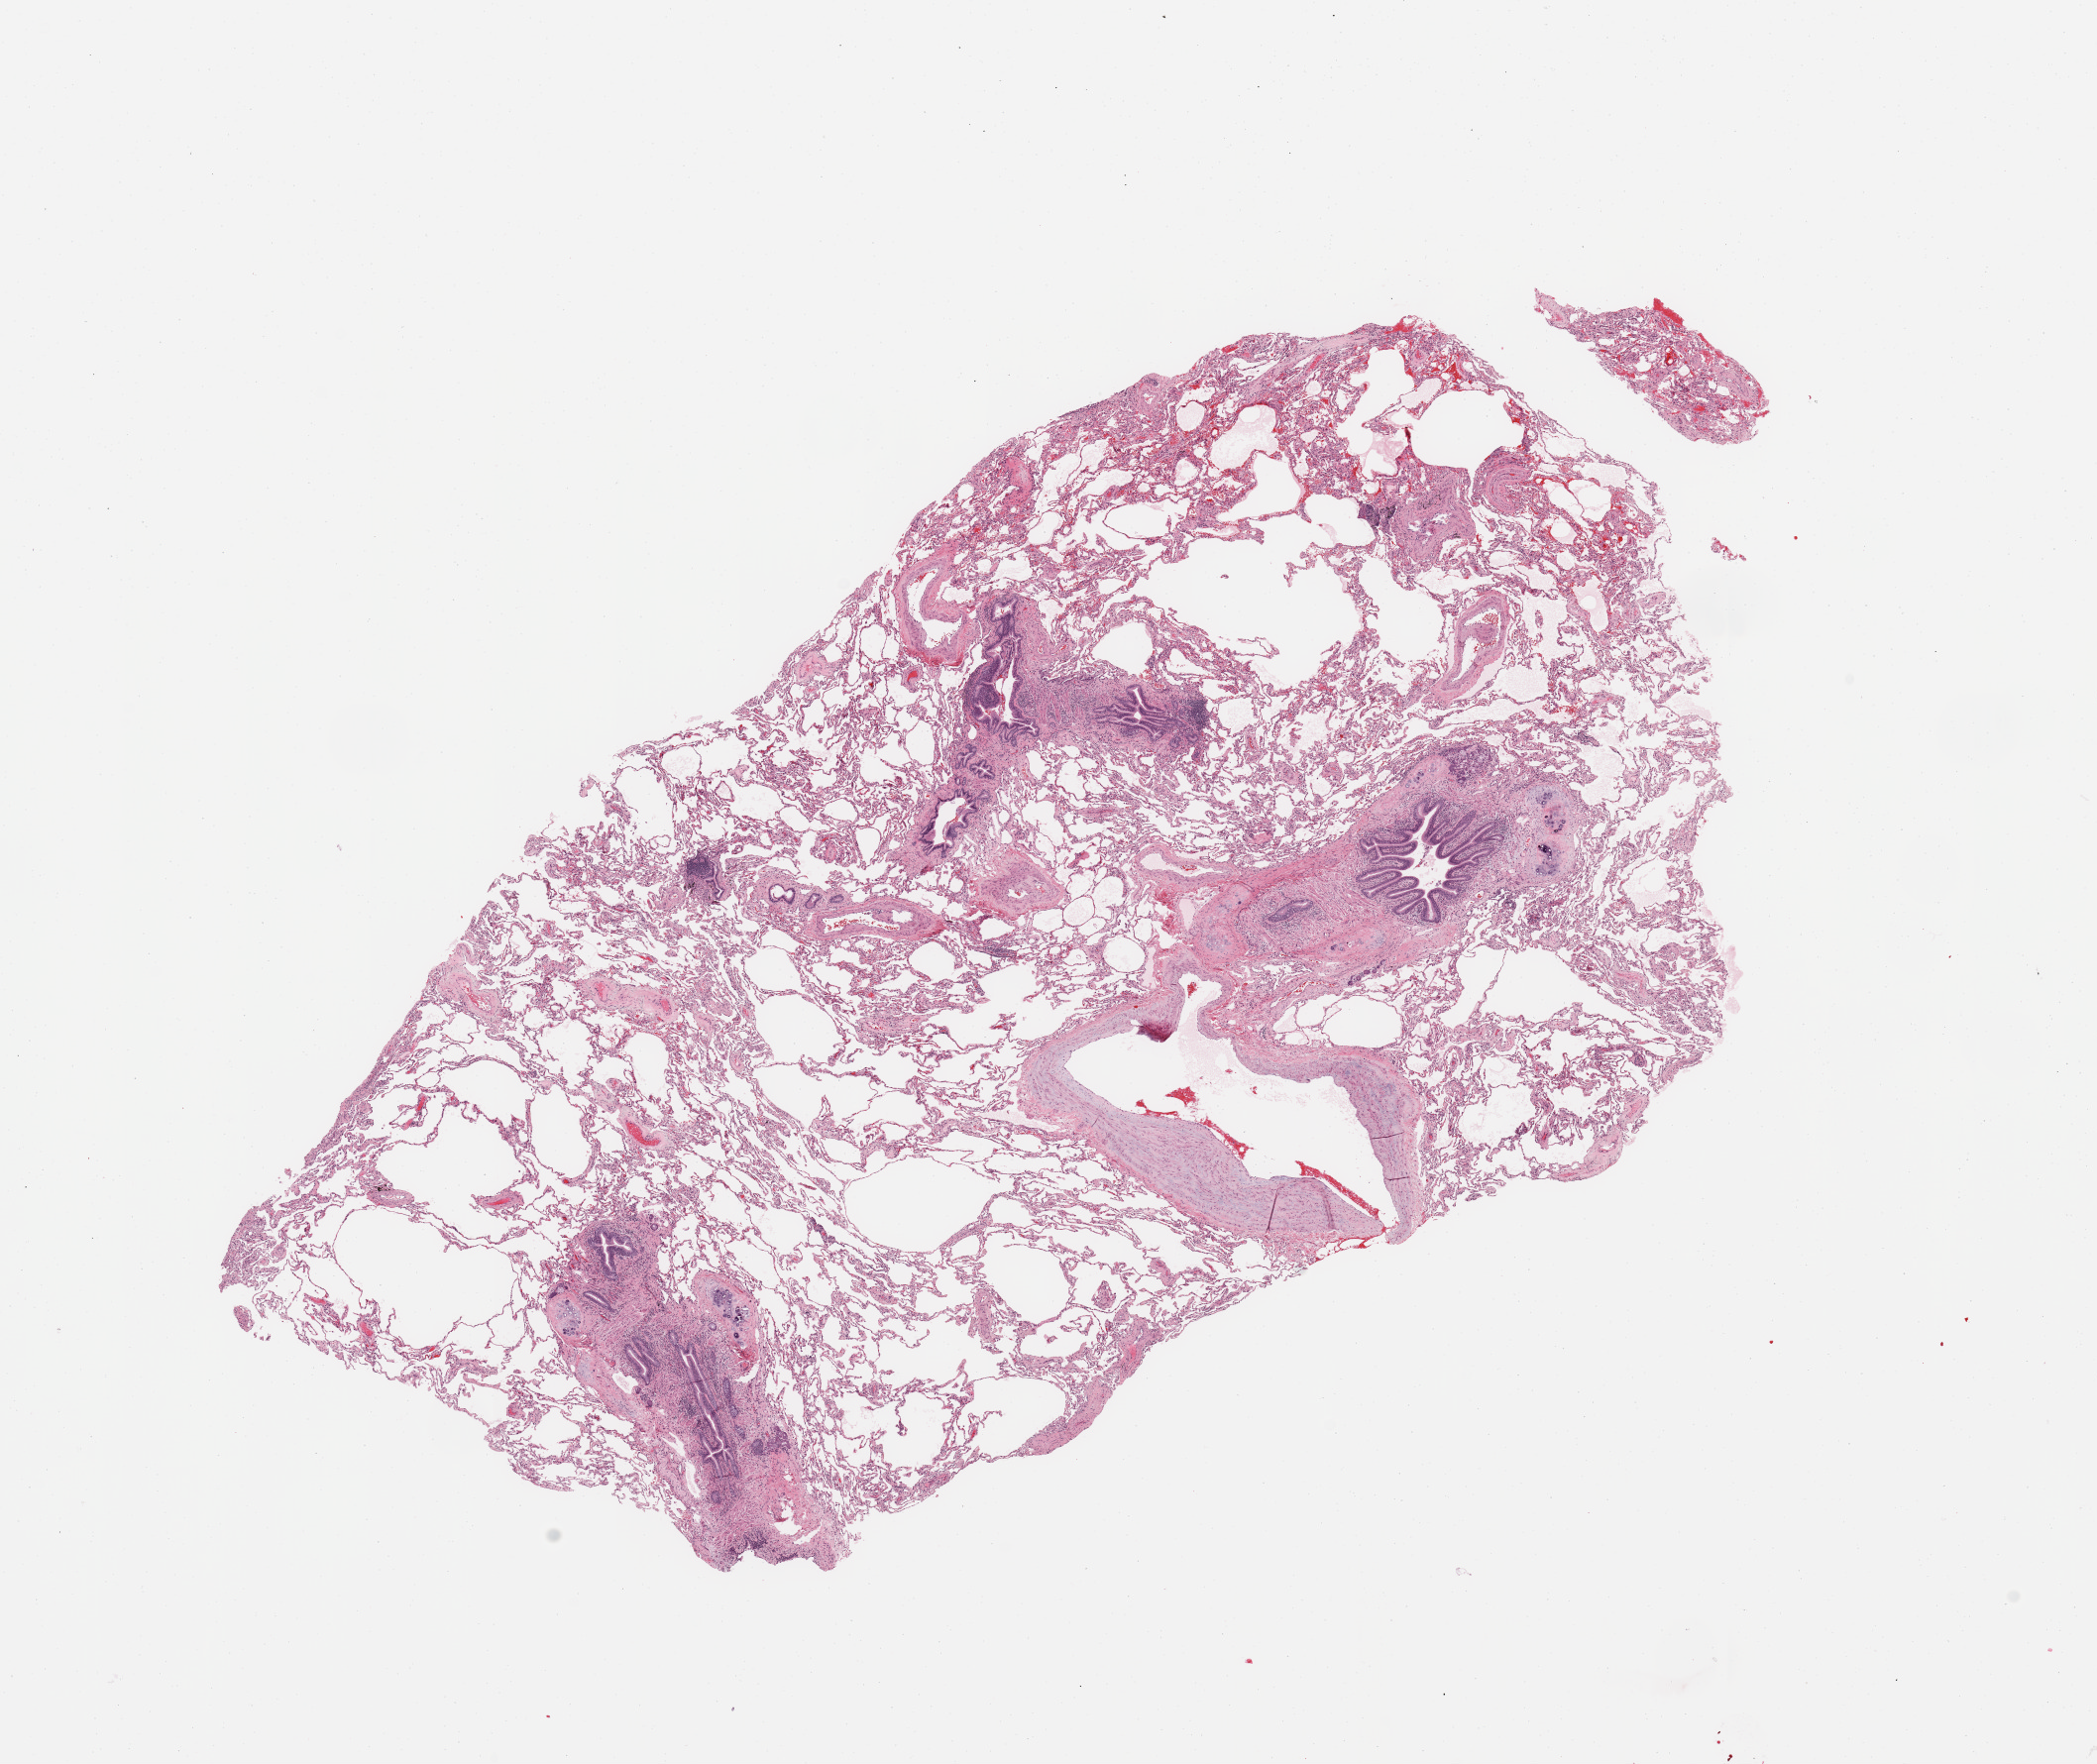
Whole-slide histology image, H&E — a low-resolution overview of the entire scanned area, about 16.7 x 14.1 mm (acquisition: 20x scan). Normal (non-tumour) tissue sample, sampled site: lung. Female, 75 y/o.
* this section: normal (non-tumour) tissue from the same patient
* patient diagnosis: Squamous cell carcinoma, NOS